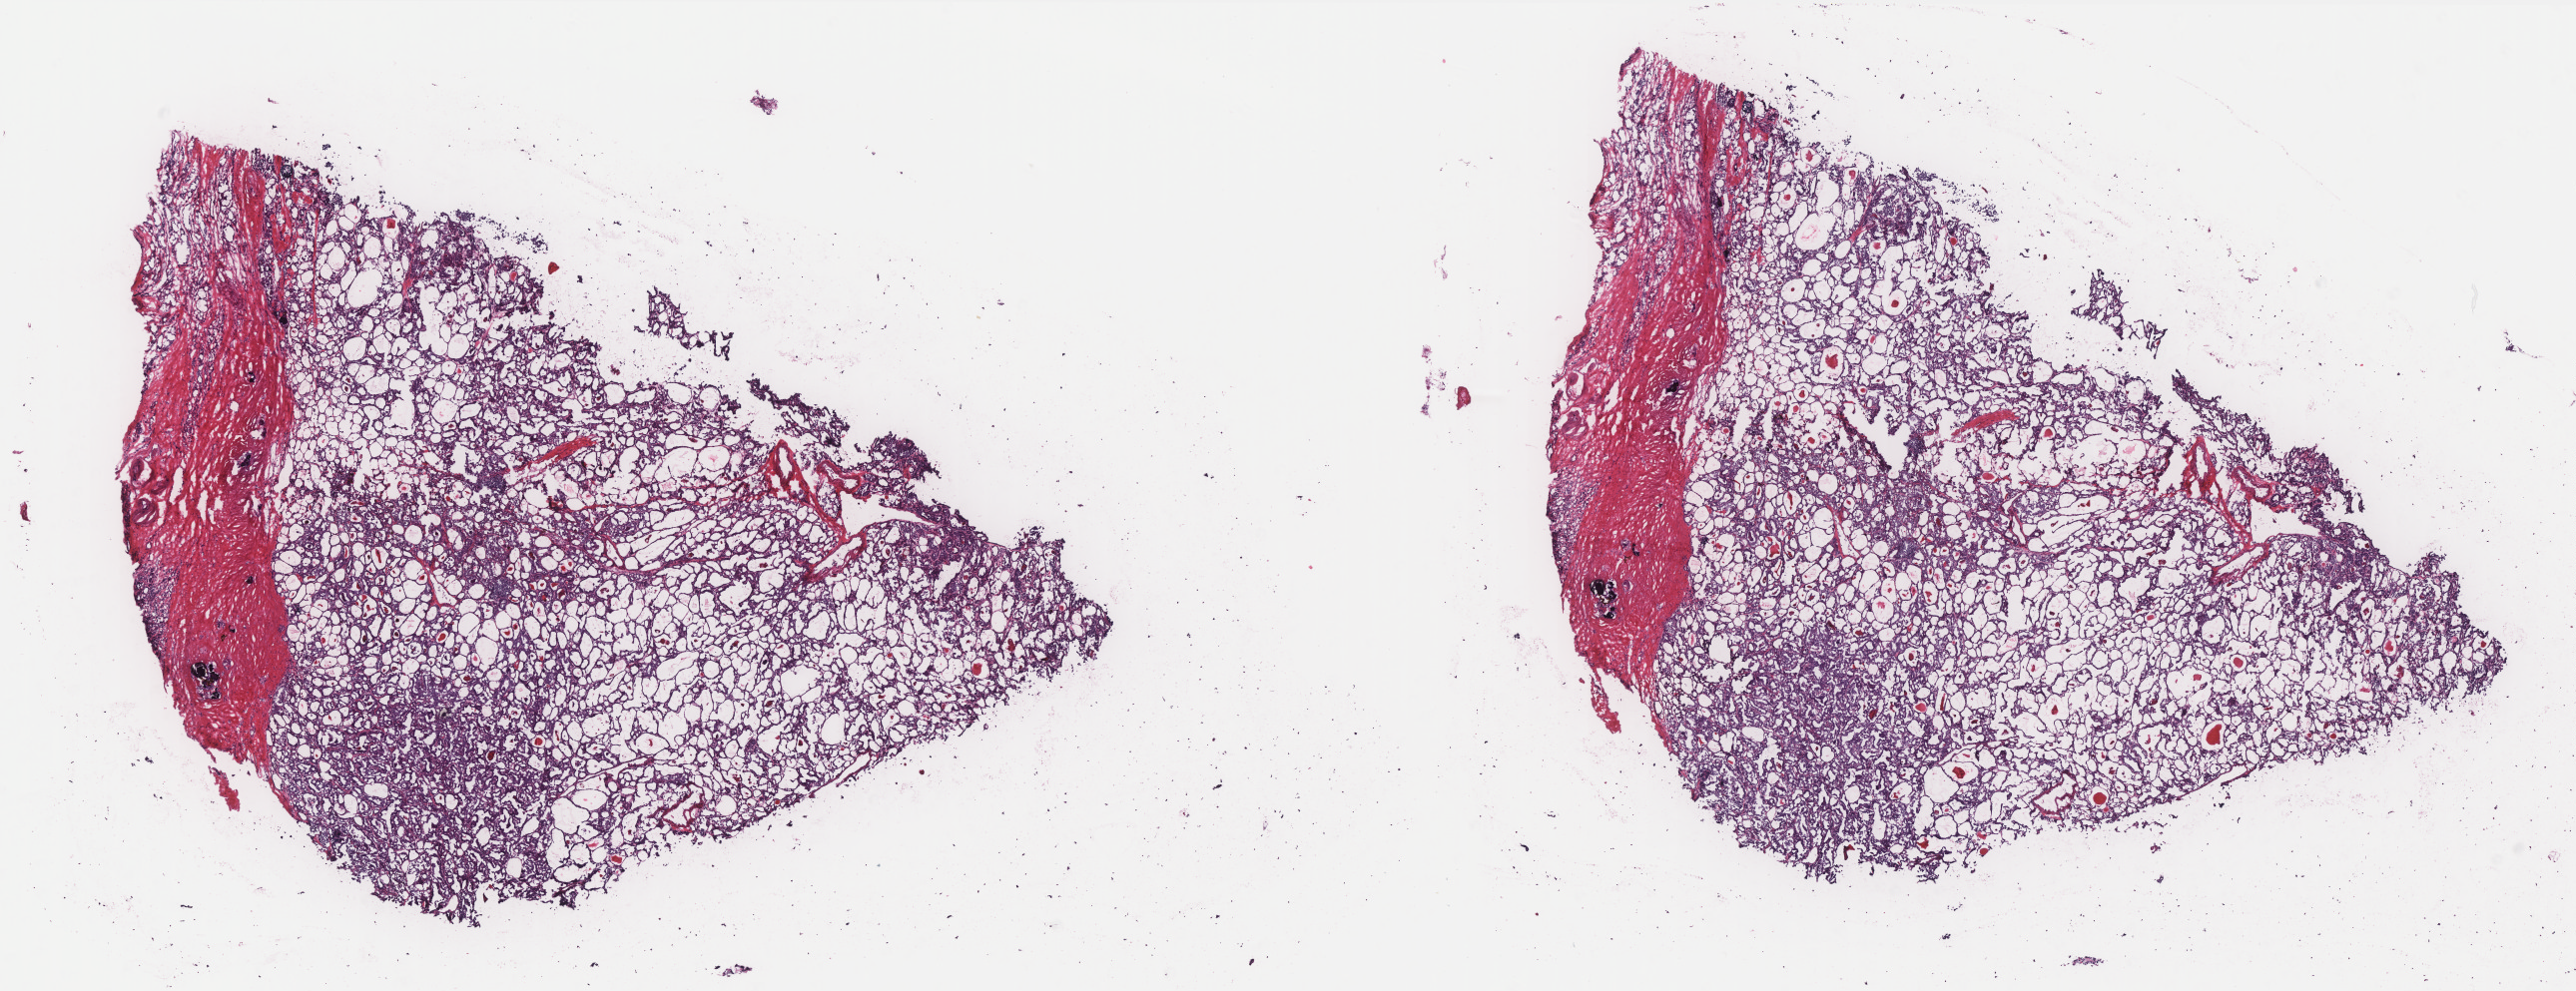
Digitized Hematoxylin and eosin (H&E) stained tissue section (whole slide), a low-resolution overview of the entire scanned area, about 20.7 x 8.0 mm. Frozen section. Primary tumour sample from the thyroid. Male, age 36 years at initial diagnosis.
Histologic diagnosis: Papillary adenocarcinoma, NOS.